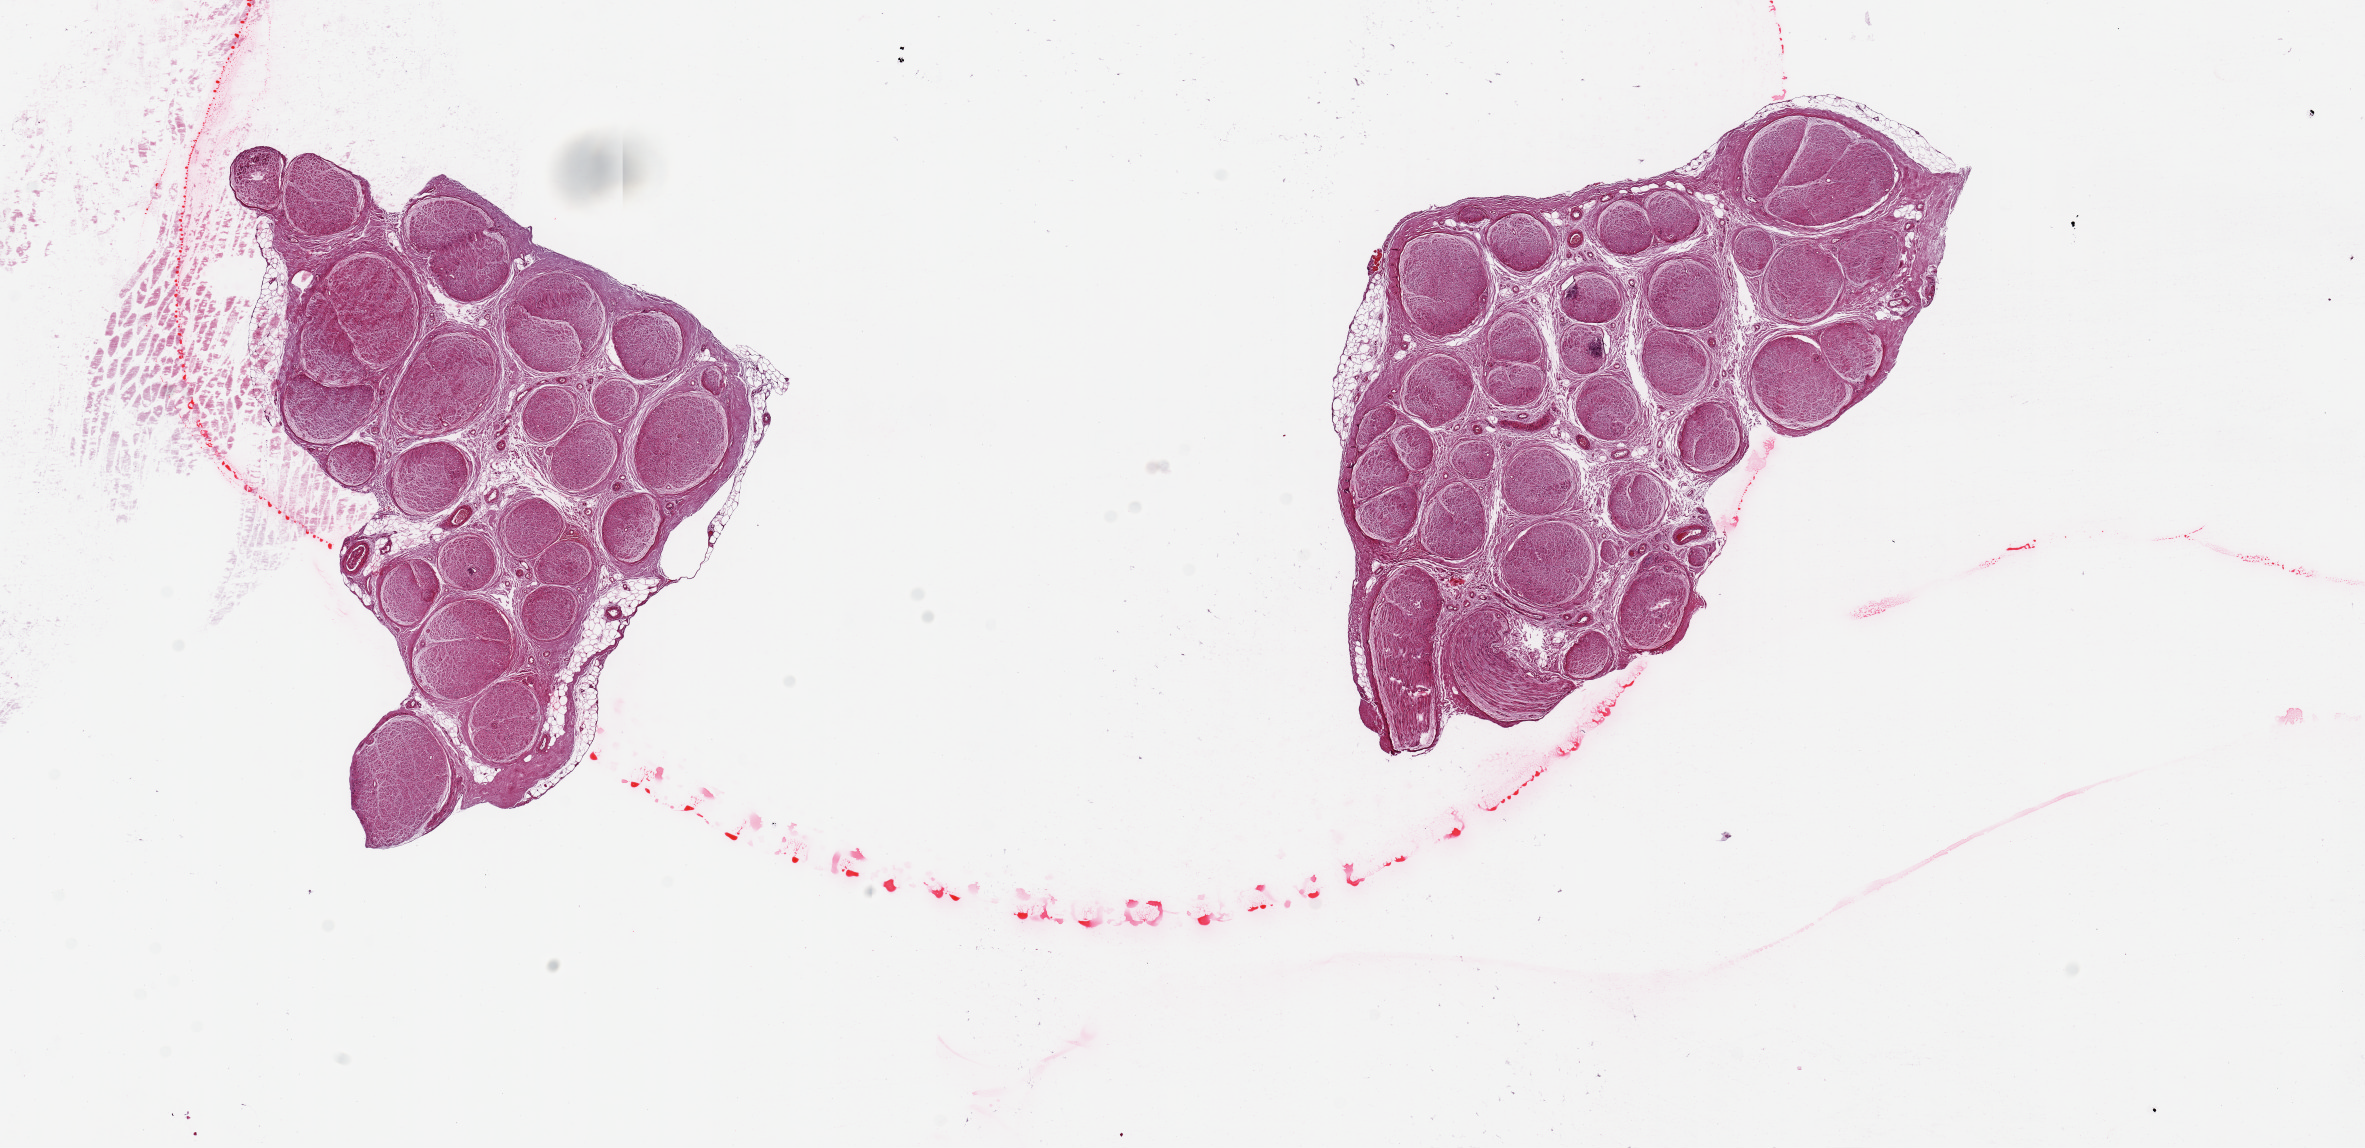
Hematoxylin and eosin (H&E) whole-slide image, brightfield, shown as a low-resolution overview of the whole scanned area (about 18.7 x 9.1 mm, acquisition: 20x scan), PAXgene-fixed, paraffin-embedded tissue, target tissue: tibial nerve, tissue donor sample. Donor sex: male.
Reviewer comment on this tissue sample: 2 pieces, 5x5 & 6x5mm; fairly clean, one iwht adherent nubbing of fat.